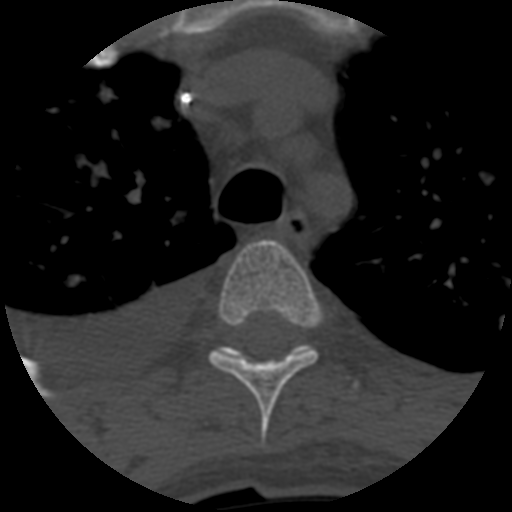
CT including the spine, one axial slice. Slice 468 of 708 in the series (ordered by position). Reconstruction kernel STANDARD. One of 3 acquisitions stored at this slice position. Bone window (W 1800 / L 400 HU). 1.25 mm slice thickness. 512 × 512 image matrix, field of view 160 × 160 mm. Patient age 55 years. Case-level facts recorded for this patient, not image findings: primary cancer: colon.
Outlined on this slice (semi-automatic segmentation, software-assisted and operator-edited):
- T3 vertebra: bounding box (x1, y1, x2, y2) in pixels: (239, 356, 241, 358)
- T4 vertebra: (208, 240, 322, 448)
- T5 vertebra: (214, 345, 358, 388)